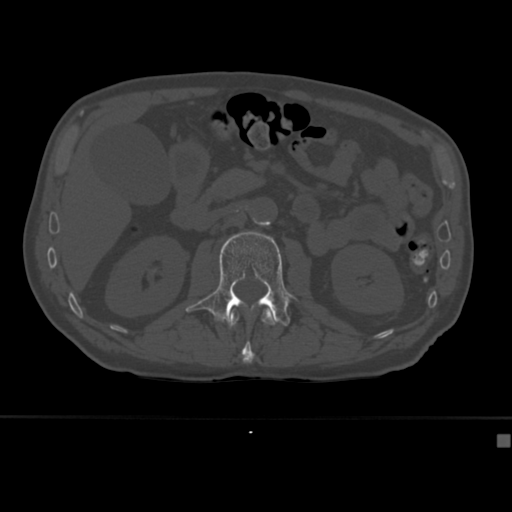
CT including the spine, one axial slice. Slice 153 of 430 in the series (ordered by position). Reconstruction kernel Br40s. 120 kVp. Bone window (W 1800 / L 400 HU). 1.5 mm slice thickness. 512 × 512 image matrix. Patient: male, 64 years. From the clinical record (not read from this slice): primary cancer: uterus; vertebrae with lytic lesions (as recorded): T1, T4, T5, T7, L5.
Annotated regions visible in this slice (semi-automatically segmented with operator editing):
- L1 vertebra: box from (x=229, y=308) to (x=276, y=364) px
- L2 vertebra: (x=186, y=231)–(x=295, y=326)